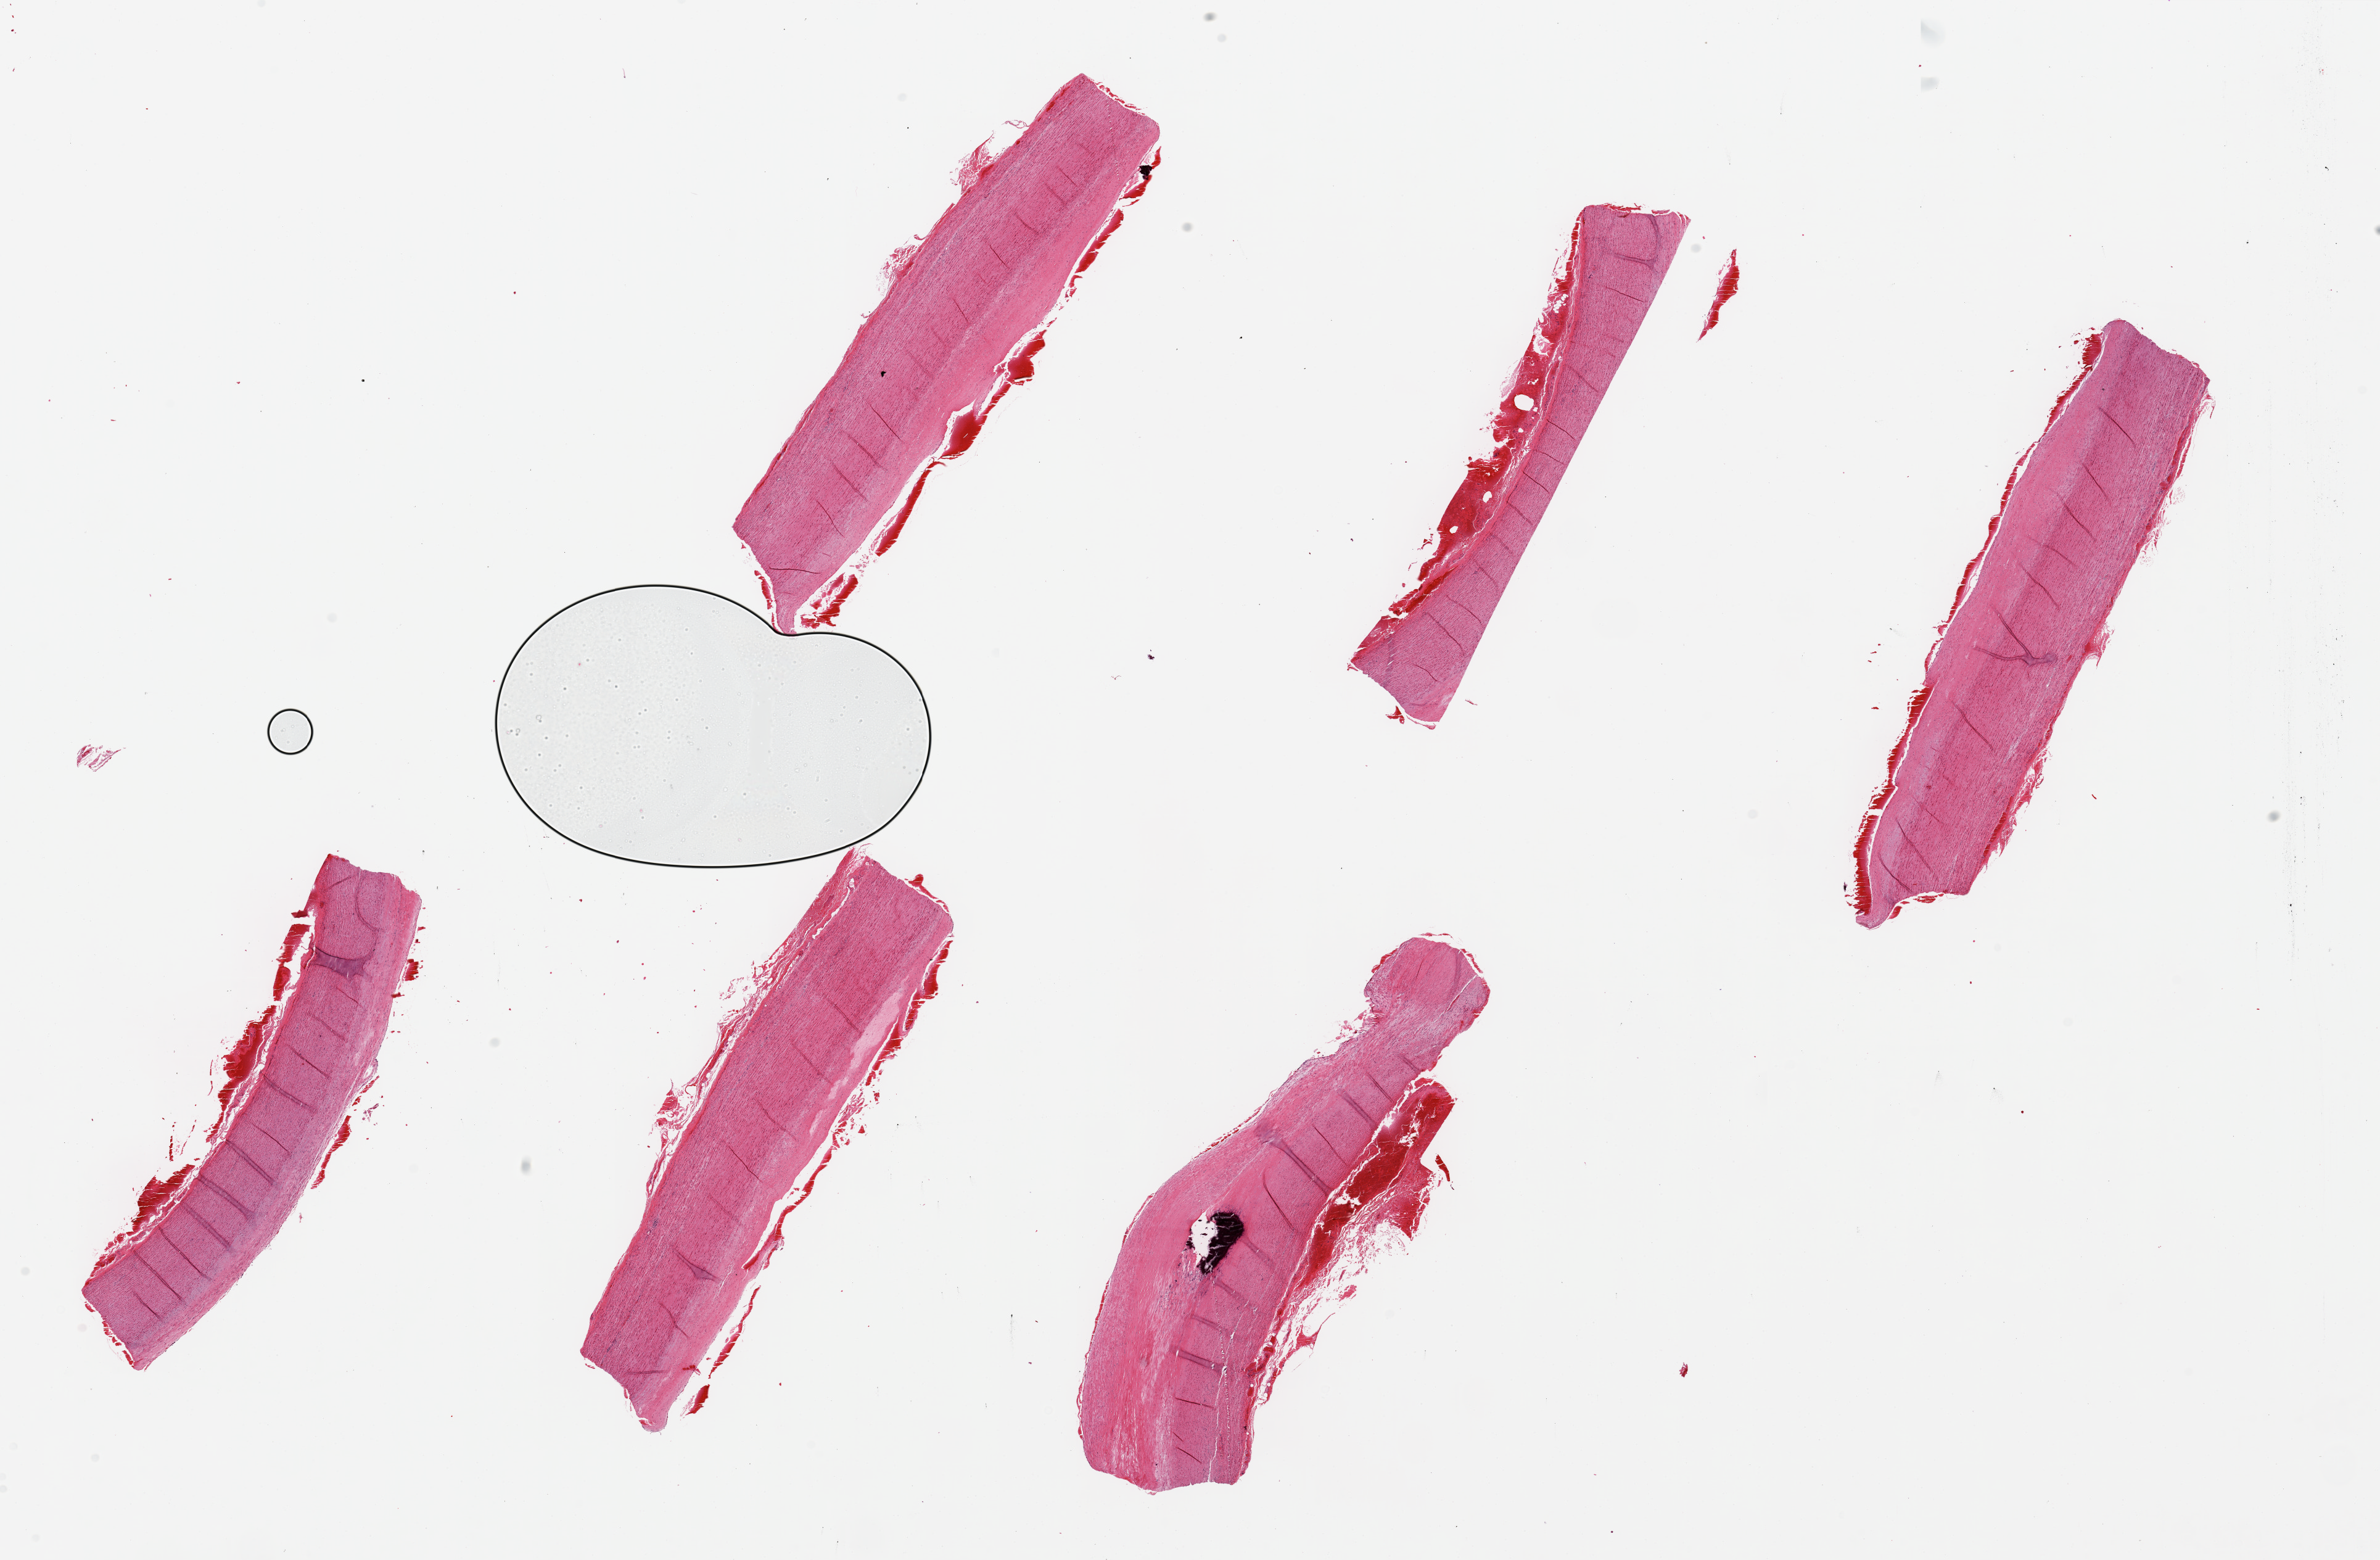
Whole-slide image, H&E stain, brightfield — low-resolution overview of the scanned area, about 30.5 x 20.0 mm, PAXgene-fixed paraffin-embedded (PFPE) section, section of aorta (target tissue), tissue donor sample. Donor: male.
Review note (as recorded): 6 pieces, up to 8x3mm; Large calcified plaque in 1. Adventitial hemorrhage.